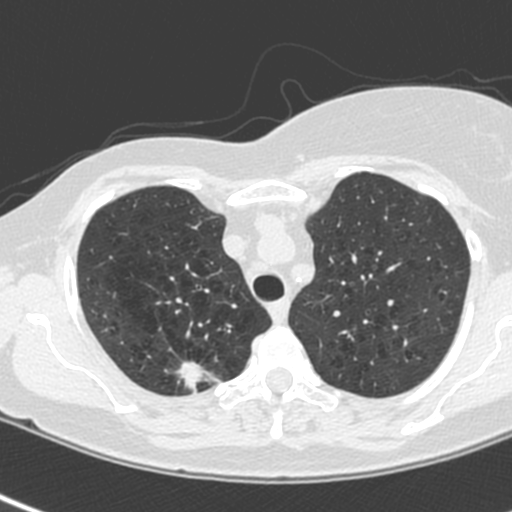
Axial slice from a low-dose chest CT screening exam, baseline annual screen, lung window (W 1500 / L -600 HU), 1.3 mm slice thickness, standard (soft-tissue) reconstruction kernel (C), slice 39 of 214 in the series, 512 × 512 image matrix. Female participant, aged 64 years at enrolment.
Expert reader's lesion annotation, bounding box [x1, y1, x2, y2] px = [166, 354, 221, 404]. The exam's reader record, not a measurement of the box and not confirmed to be the same lesion: non-calcified nodule or mass ≥4 mm, right upper lobe, 13 × 10 mm, spiculated (stellate) margins, soft tissue attenuation. Official screen result: positive, change unspecified: nodule(s) >= 4 mm or enlarging nodule(s), mass(es), or other non-specific abnormalities suspicious for lung cancer. Lung cancer was diagnosed 21 days after this screen: adenocarcinoma, NOS, right upper lobe, poorly differentiated (G3), stage IIIB (AJCC 6th edition), 20 mm at pathology.